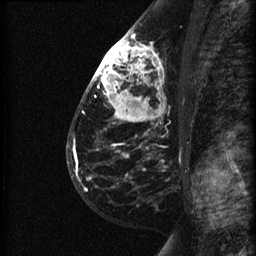
Breast MRI (dynamic contrast-enhanced), one sagittal slice; dynamic contrast-enhanced series, image 2 of 3 at this slice position (ordered by acquisition); 1.5 T; TE 4.2 ms, TR 22.7 ms; 1.5 mm slice thickness; 256 × 256 image matrix, field of view 180 × 180 mm. Patient: female, 48 years. From the clinical record (not read from this slice): setting: breast cancer imaged before/during neoadjuvant chemotherapy; receptor status: triple-negative.
Structures marked on this image (semi-automatic segmentation, software-assisted and operator-edited):
- analysis volume of interest (the breast-tissue region the enhancement analysis was run in; not a lesion): bounding box (x1, y1, x2, y2) in pixels: (89, 27, 190, 180)
- tumour enhancement mask (voxels above the 90 % enhancement threshold inside the analysis volume of interest): (92, 32, 161, 157)